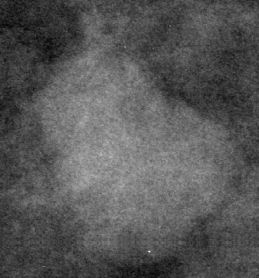
Crop from a digitized film mammogram around one marked abnormality, left breast, CC view, BI-RADS breast density category 2 (scale 1–4).
Finding: mass, shape lobulated, margins circumscribed; BI-RADS assessment category 3; subtlety rating 4 on a 1 (subtle) to 5 (obvious) scale; pathology (as recorded): benign.